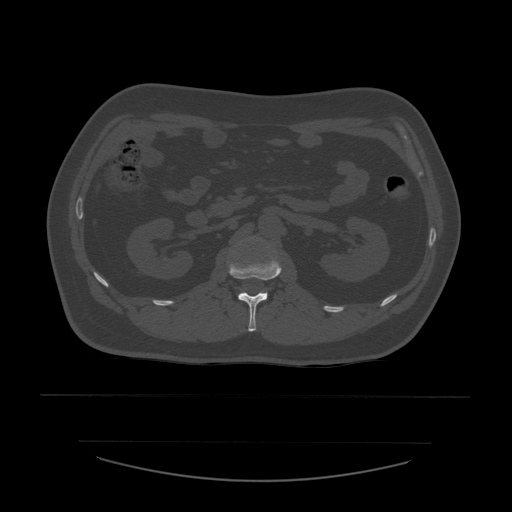
CT including the spine, one axial slice; slice 219 of 532 in the series (ordered by position); 120 kVp; bone window (W 1800 / L 400 HU); 512 × 512 image matrix, field of view 441 × 441 mm. Patient age 44 years. From the clinical record (not read from this slice): primary cancer: soft tissue sarcoma.
Outlined on this slice (semi-automatic segmentation, software-assisted and operator-edited):
- L1 vertebra: box from (x=229, y=255) to (x=282, y=332) px